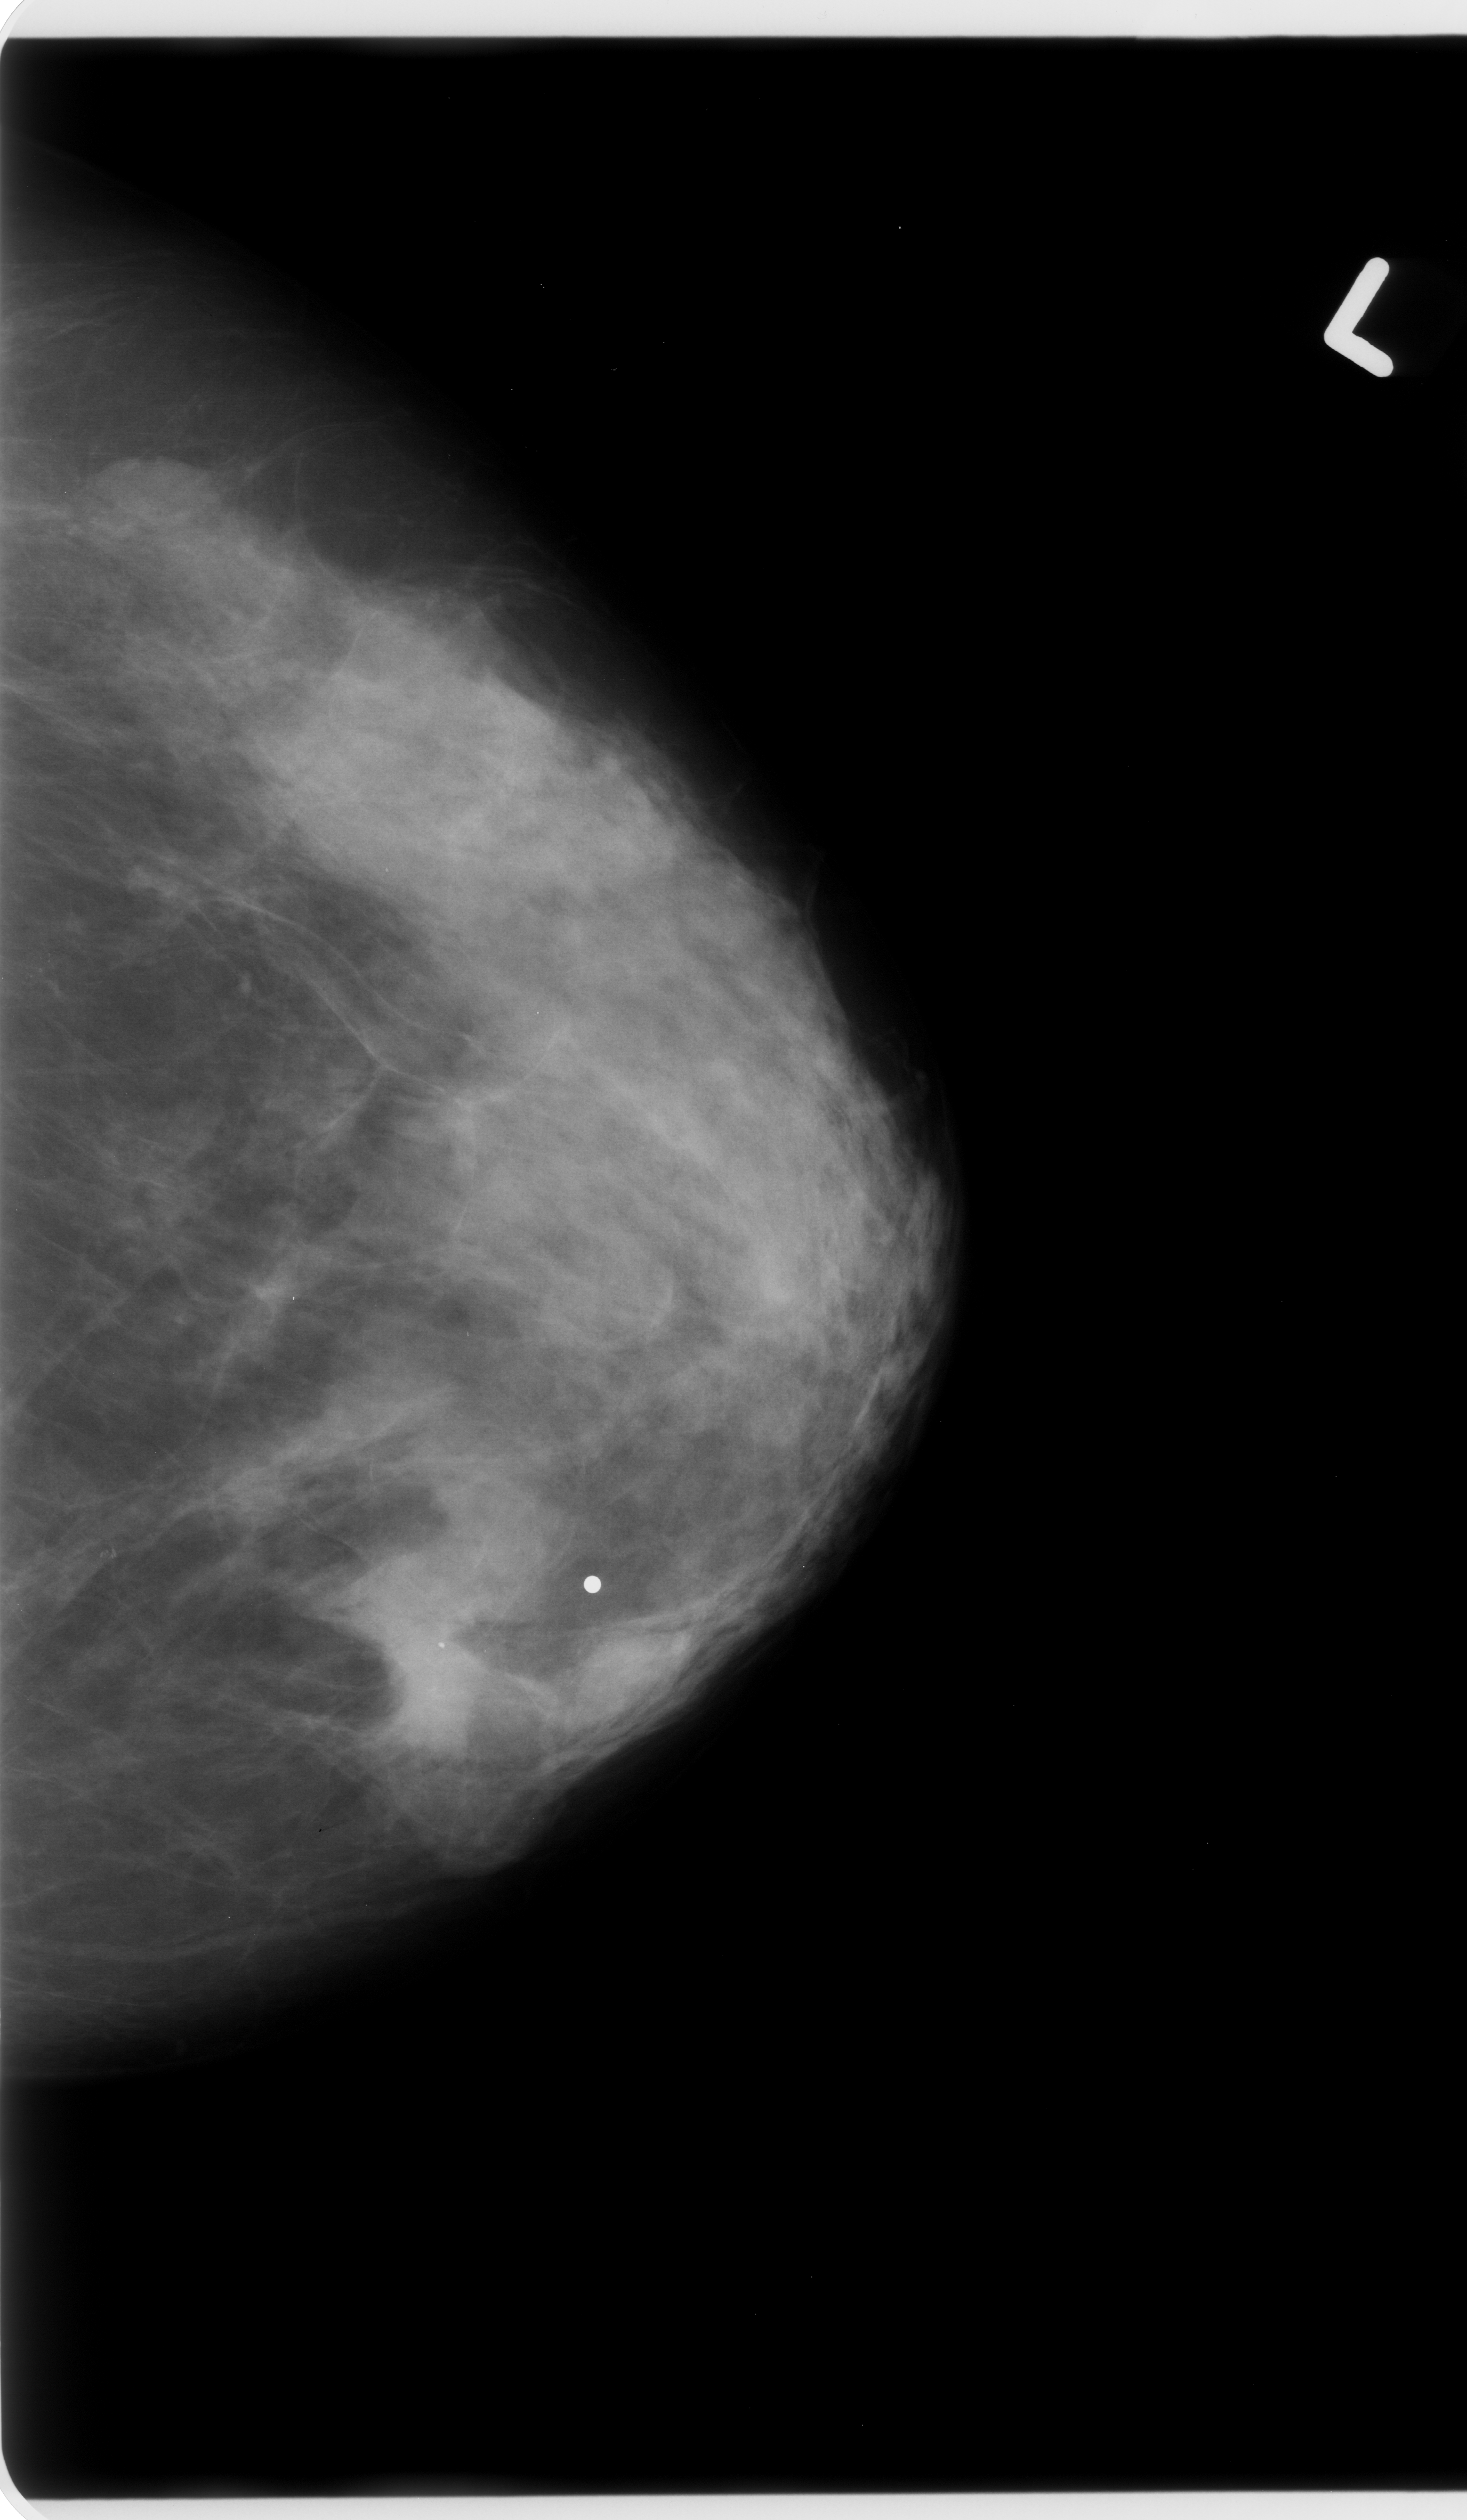
Digitized screen-film mammogram, left breast, craniocaudal (CC) view, BI-RADS breast density category 3 (scale 1–4).
Finding: mass, shape irregular, margins ill defined; BI-RADS assessment category 5; pathology (as recorded): malignant.